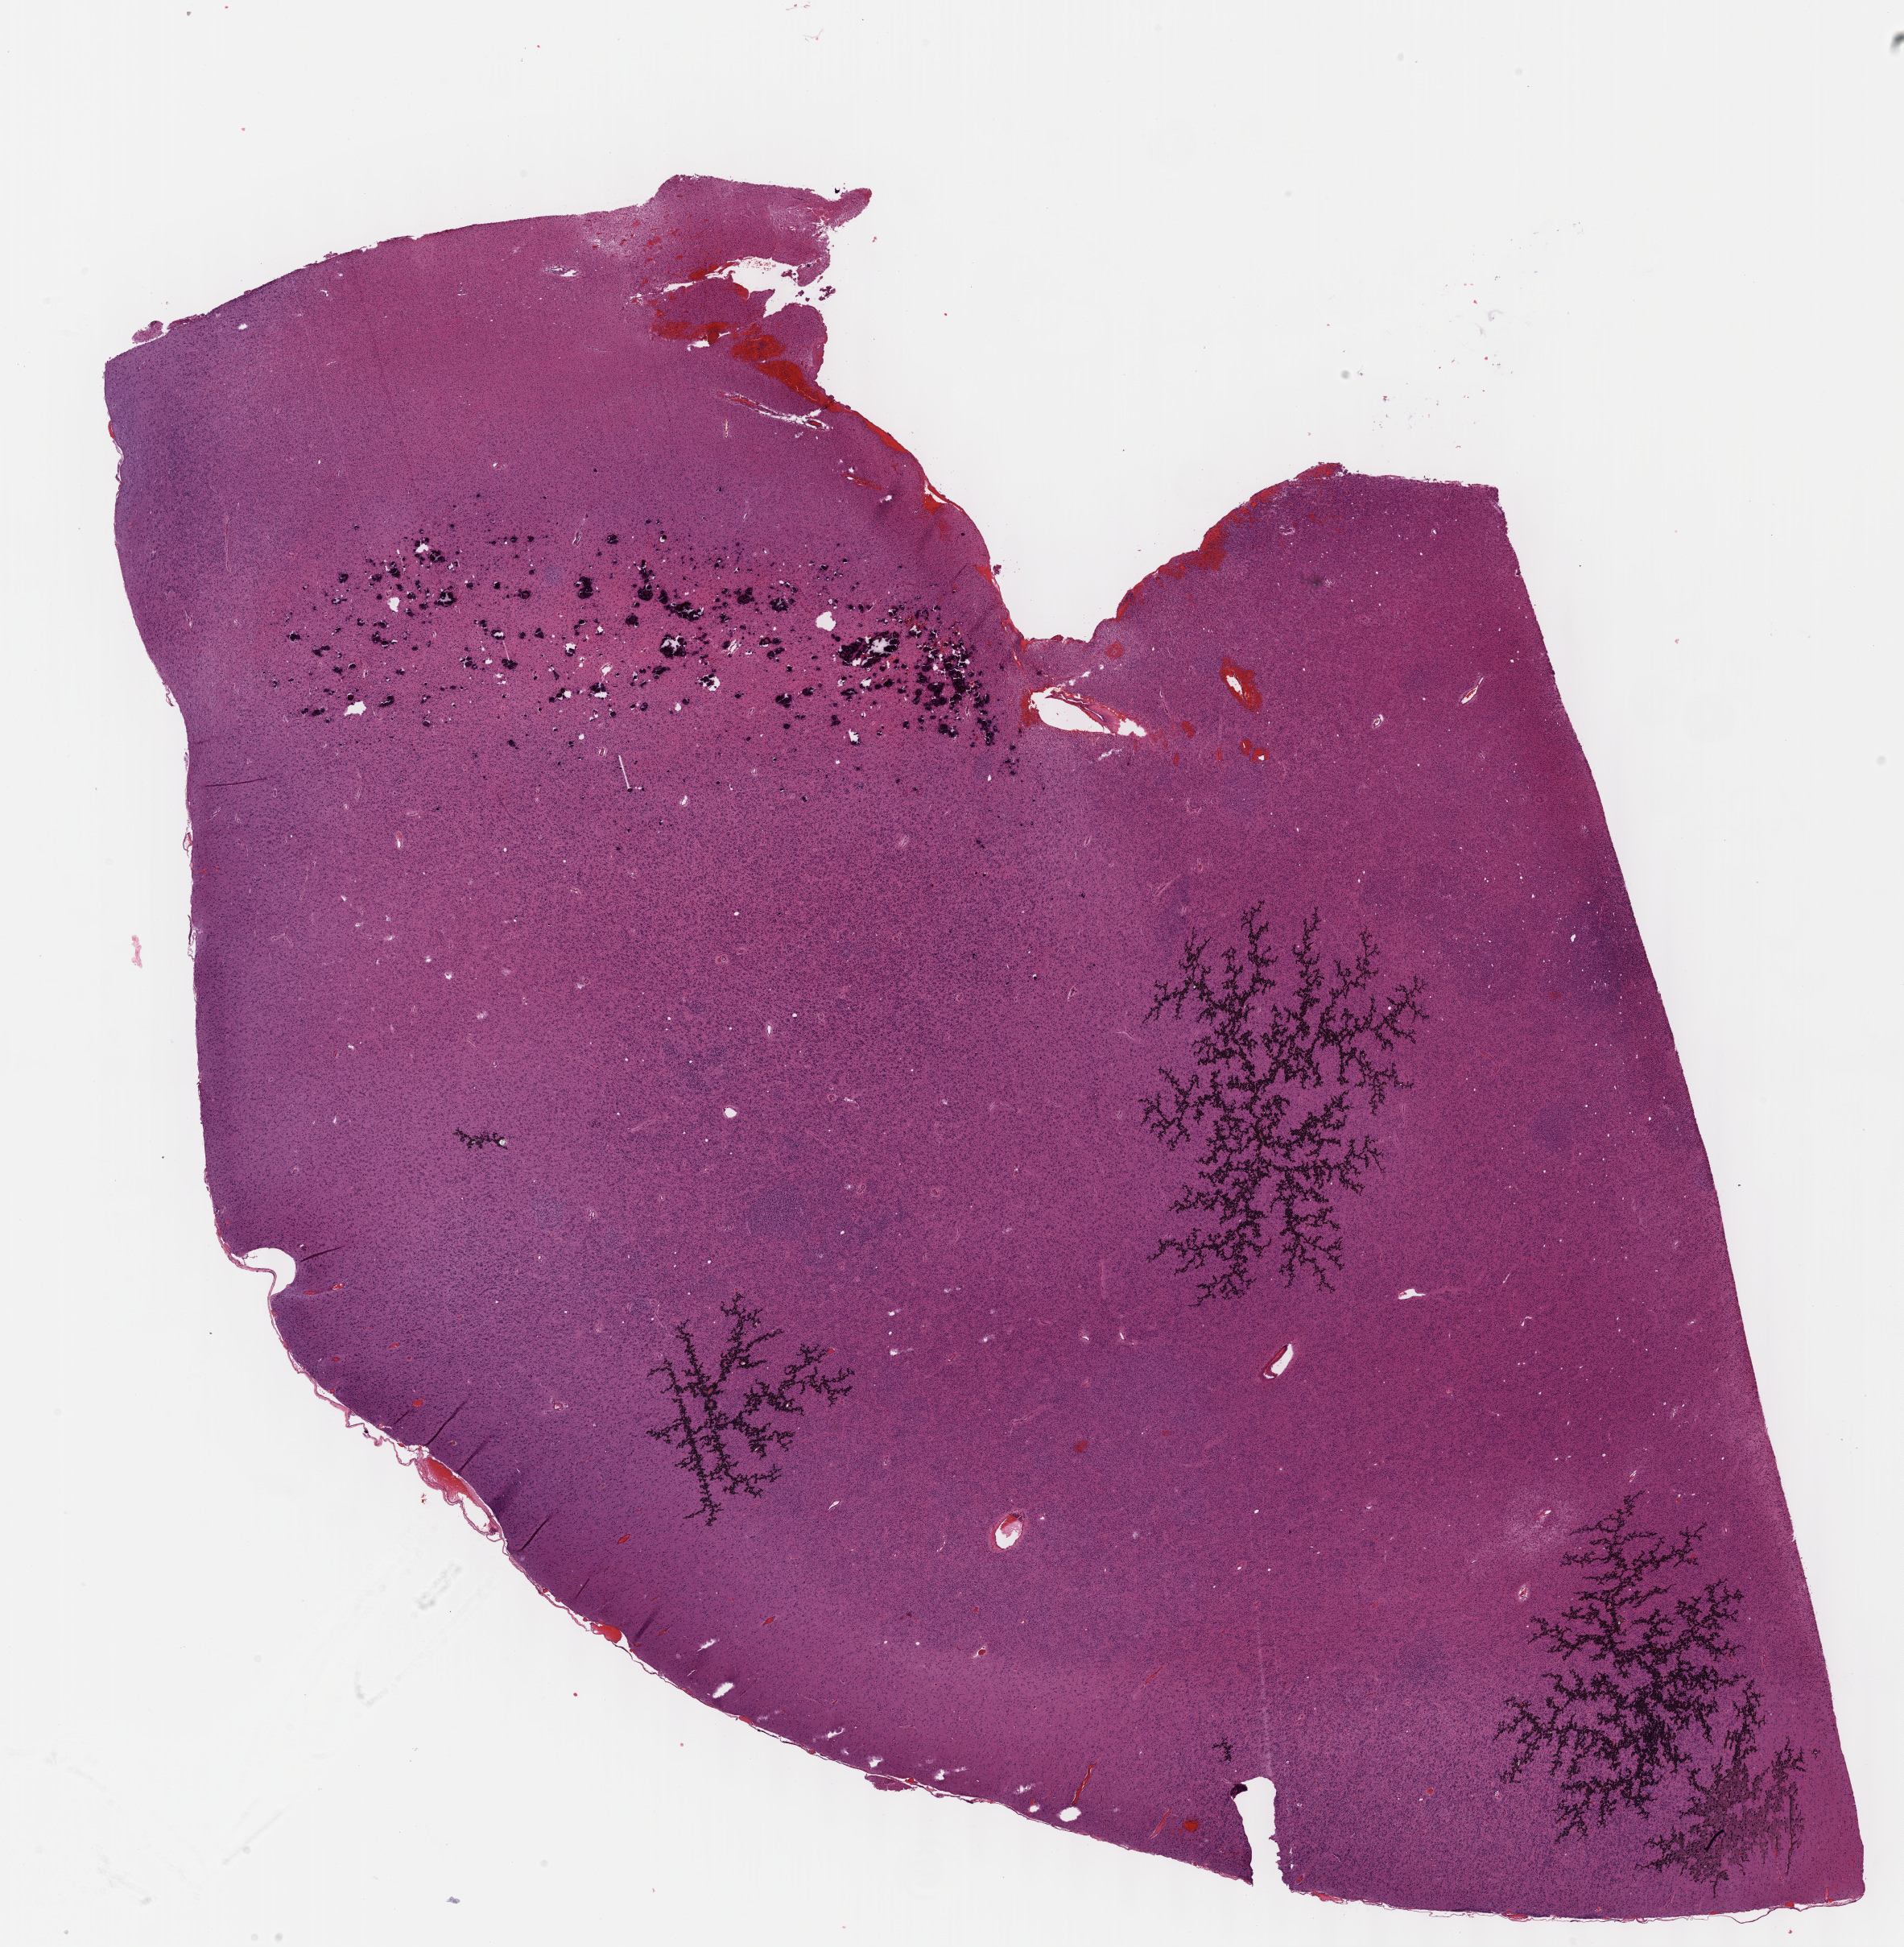
Whole-slide histology image, H&E-stained — whole scanned area (about 19.1 x 19.5 mm, slide scanned at 40x) shown as a low-resolution overview, formalin-fixed paraffin-embedded (FFPE) diagnostic section, brain, primary tumour sample. Male, age 64 years at initial diagnosis.
Diagnosis: Oligodendroglioma, anaplastic (cerebrum).